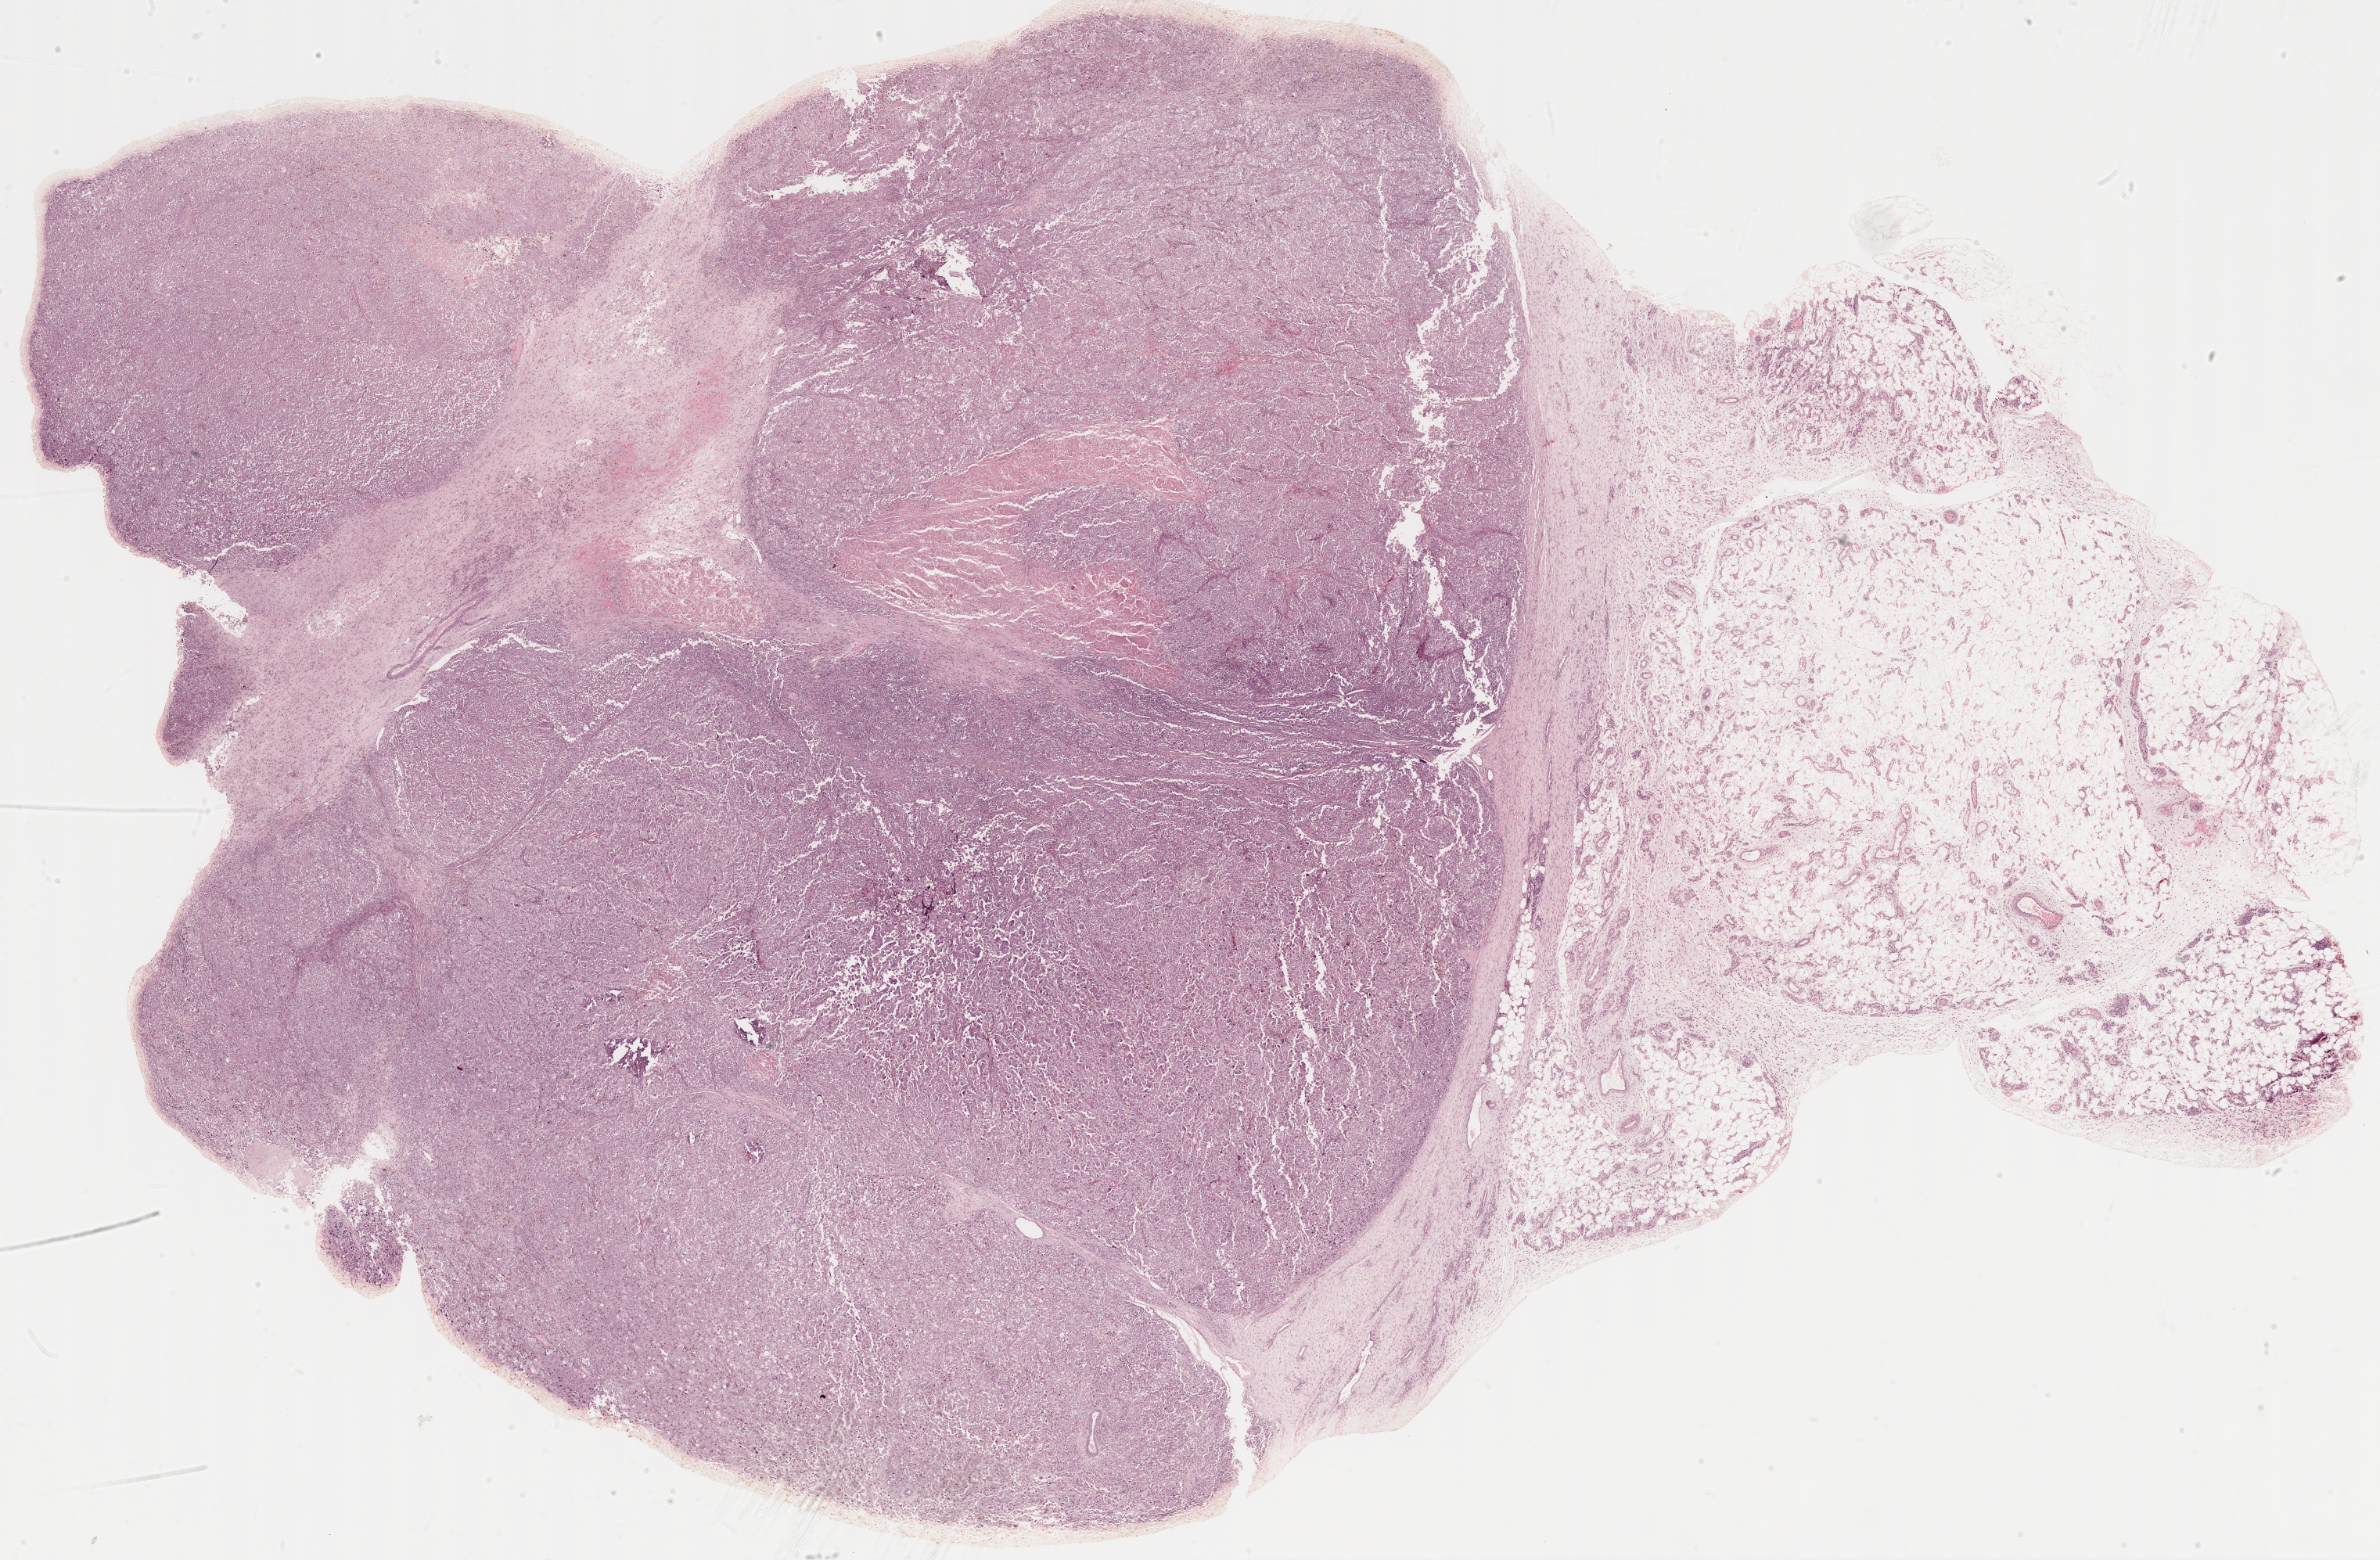
H&E whole-slide image, a low-resolution overview of the entire scanned area, about 24.5 x 16.1 mm. Formalin-fixed paraffin-embedded (FFPE) diagnostic section. Metastatic tumour sample. Patient: male, age at initial diagnosis 65 years.
- this section: metastatic tumour tissue
- patient diagnosis: Malignant melanoma, NOS